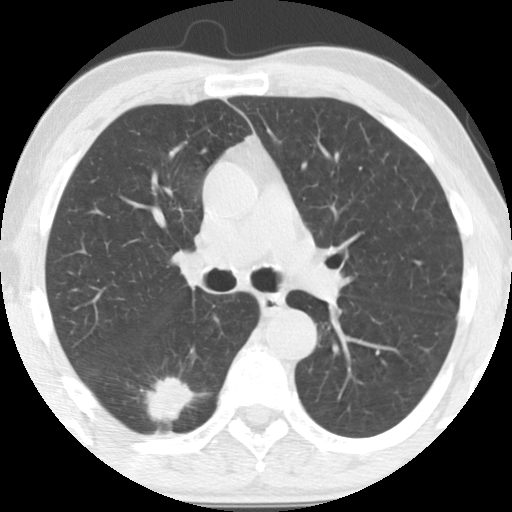
Low-dose screening chest CT, one axial slice. Slice 88 of 135 in the series (ordered by position). Reconstruction kernel STANDARD. 120 kVp. Lung window (W 1500 / L -600 HU). 2.5 mm slice thickness. 512 × 512 image matrix, field of view 300 × 300 mm.
Annotated regions visible in this slice (expert manual segmentation):
- lesion 1 (tumor, lower lobe of right lung): bounding box <147,377,194,422> (left, top, right, bottom; pixels)